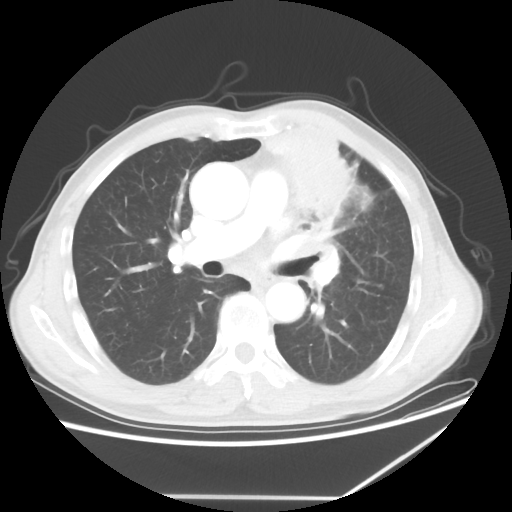
Chest CT, one axial slice; slice 36 of 64 in the series (ordered by position); lung window (W 1500 / L -600 HU); 5 mm slice thickness; 512 × 512 image matrix, field of view 383 × 383 mm. Male patient, age 64 years. From the clinical record (not read from this slice): clinical TNM (as recorded): T1c N1 M1; histopathological grade: G2.
Outlined on this slice (rectangle marked by the reading radiologist):
- lung tumour (recorded histology: squamous cell carcinoma): bounding box [x1, y1, x2, y2] px = [257, 115, 392, 238]